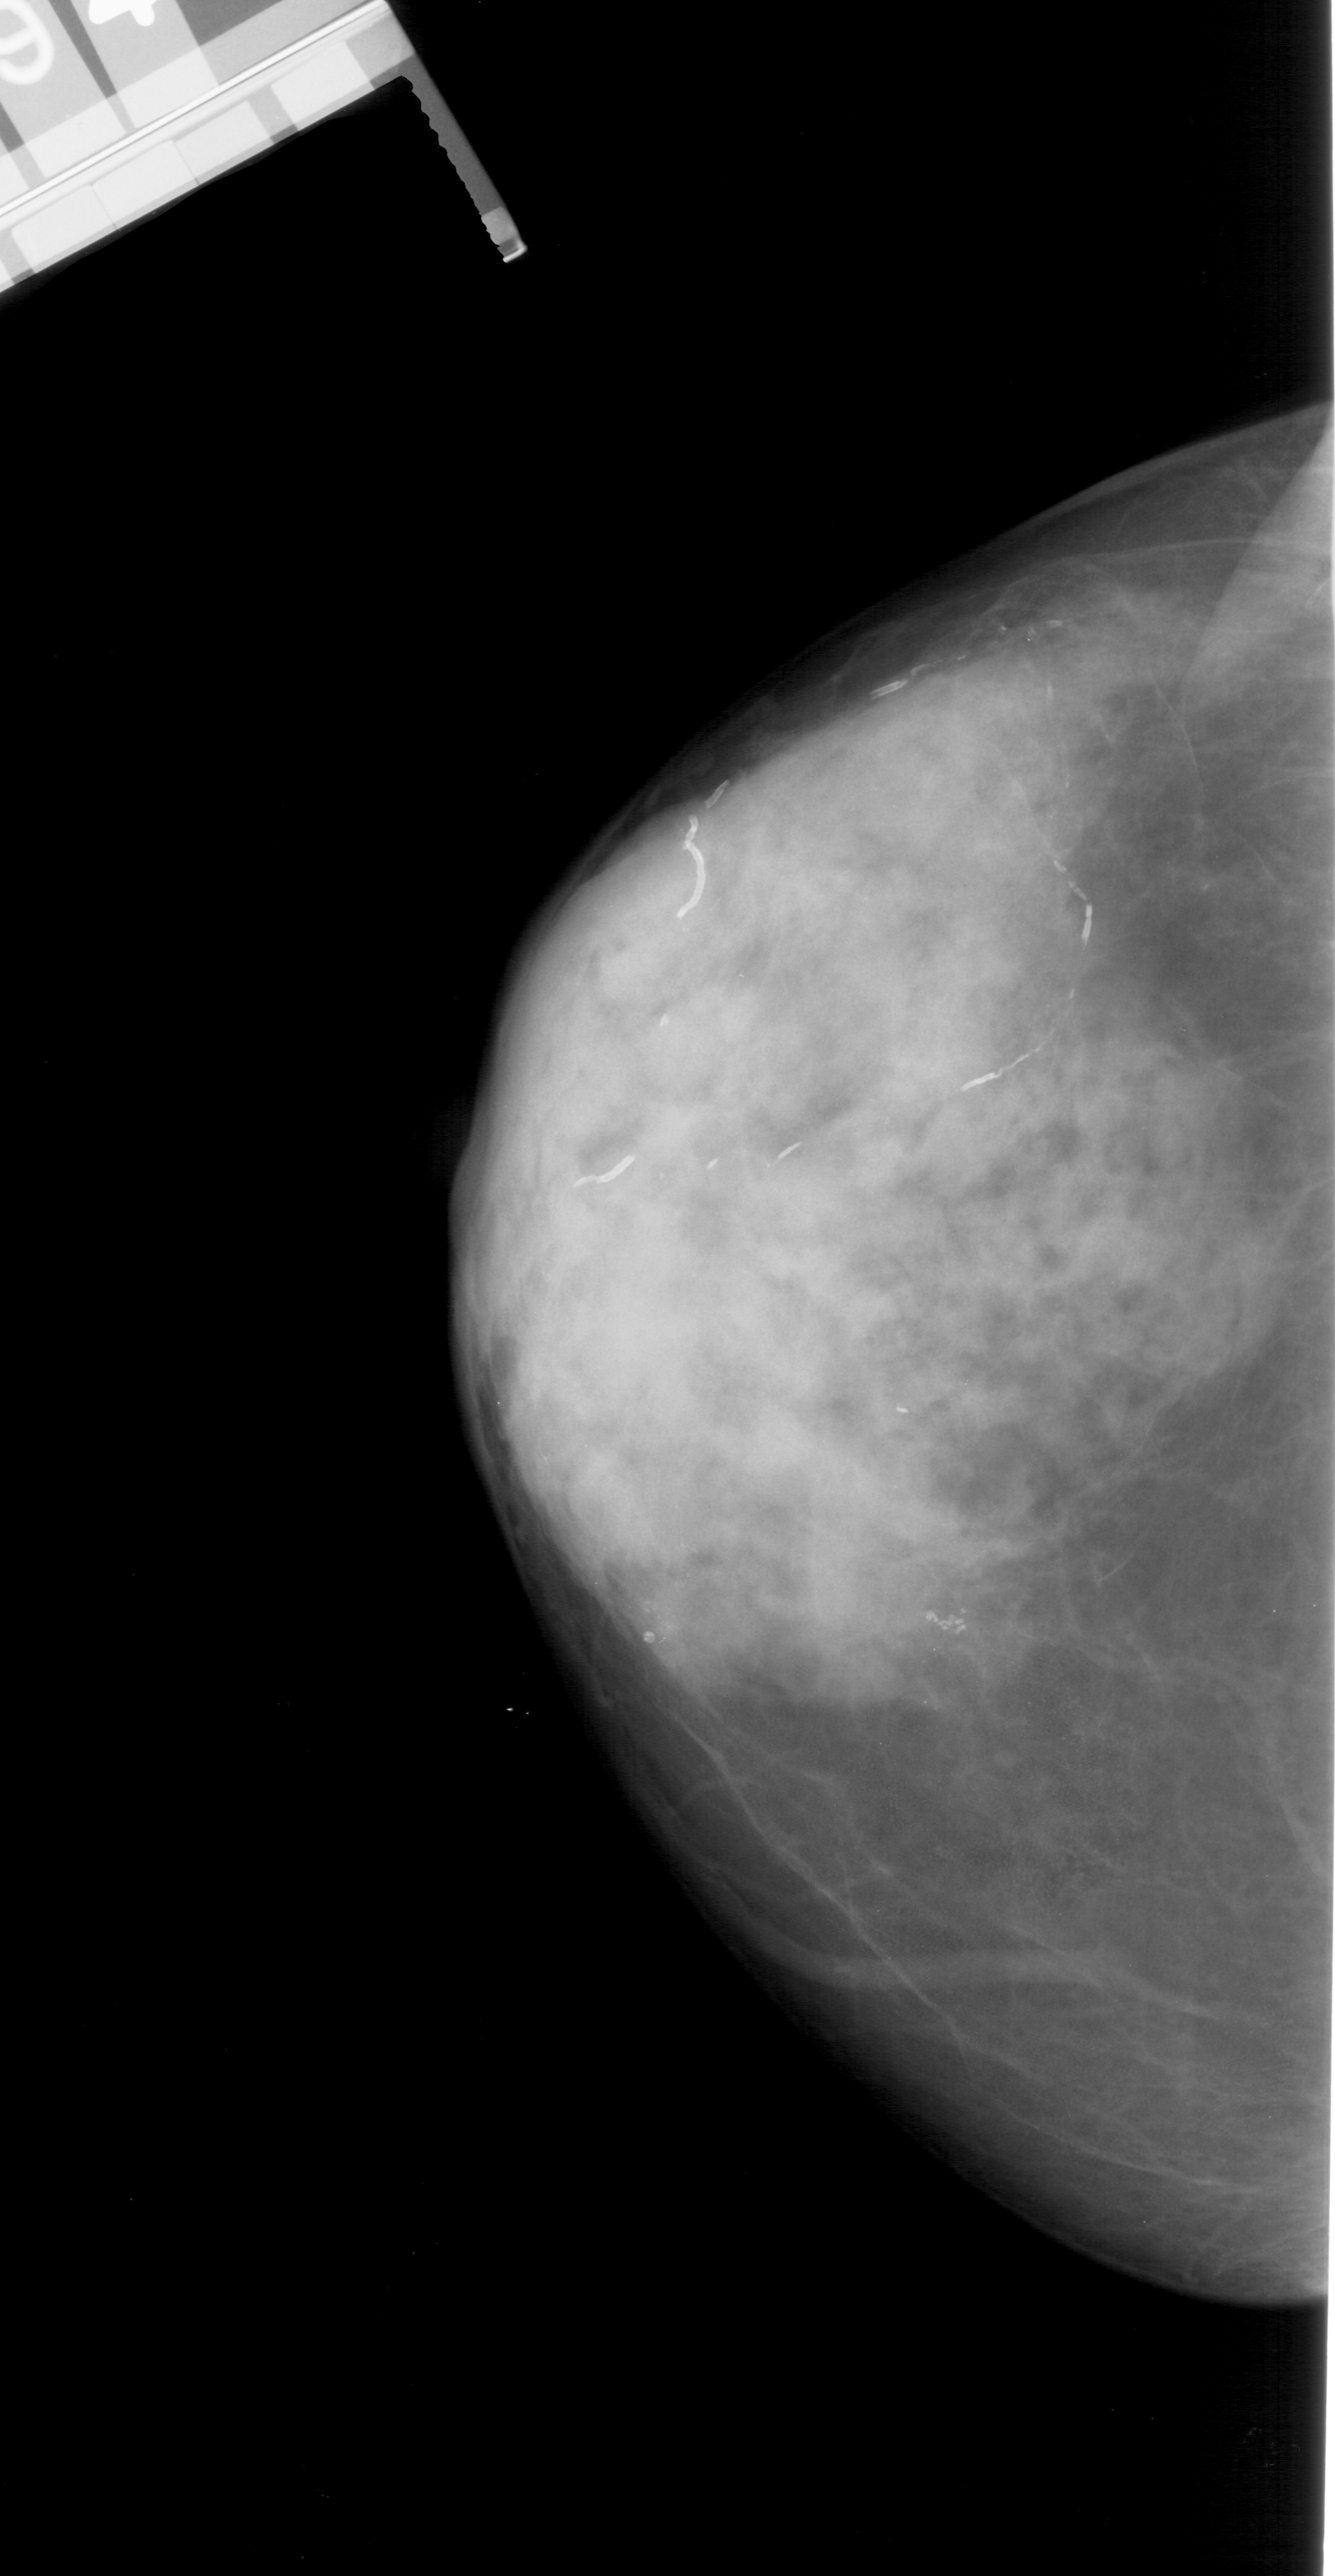
Mammogram (digitized film); left breast; craniocaudal (CC) view; BI-RADS breast density category 4 (scale 1–4); 1335 × 2576 image matrix.
Marked abnormalities (boxes around the expert regions of interest):
- calcifications, morphology pleomorphic, distribution clustered; BI-RADS assessment category 4; subtlety rating 4 on a 1 (subtle) to 5 (obvious) scale; pathology (as recorded): malignant: box from (x=878, y=1637) to (x=1011, y=1737) px